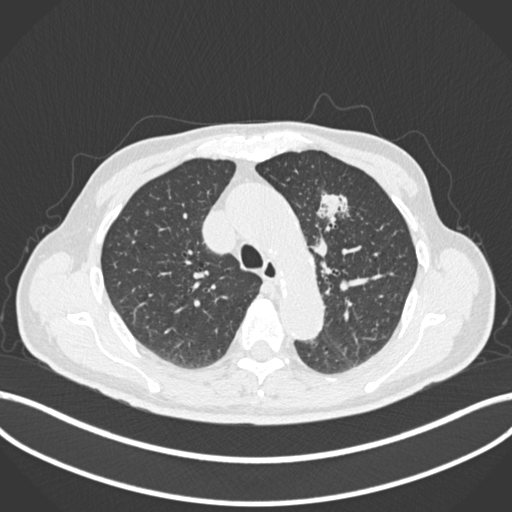
Chest CT, one axial slice; position 179 of 261 along the scan axis; 120 kVp; lung window (W 1500 / L -600 HU); 1 mm slice thickness; 512 × 512 image matrix, field of view 400 × 400 mm. Patient: male, 74 years. From the clinical record (not read from this slice): clinical TNM (as recorded): T2b N0 M1c.
Outlined on this slice (bounding box drawn by a radiologist):
- lung tumour (recorded histology: adenocarcinoma): bounding box [x1, y1, x2, y2] px = [313, 188, 355, 227]